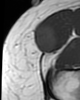
MRI of an extremity soft-tissue mass, one axial slice. Position 14 of 46 along the scan axis. MR volume resampled by the dataset authors to the PET/CT grid (not the native acquisition matrix). 3.27 mm slice thickness. 80 × 100 image matrix, field of view 78 × 98 mm. Female patient. Case-level facts recorded for this patient, not image findings: histological type: synovial sarcoma; grade: intermediate; site of the primary tumour: right thigh.
Annotated regions visible in this slice (expert contour drawn on MRI and transferred to this co-registered scan by the dataset authors):
- gross tumour volume including surrounding oedema: box from (x=34, y=26) to (x=56, y=54) px
- gross tumour volume (mass): (x=34, y=26)–(x=56, y=54)